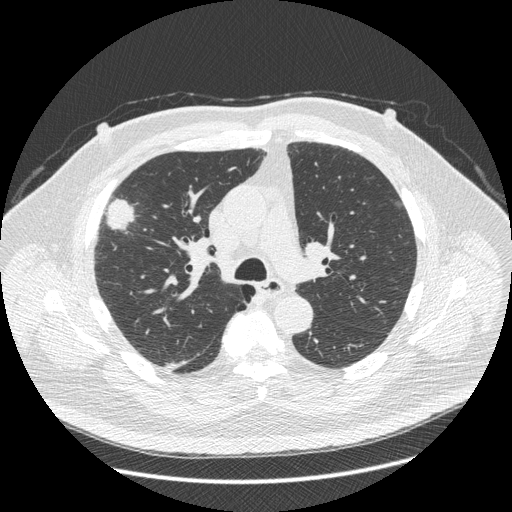
Chest CT (low-dose screening protocol), one axial image; third annual screen; lung window (W 1500 / L -600 HU); standard (soft-tissue) reconstruction kernel (STANDARD); slice 150 of 426 in the series; 512 × 512 image matrix. Male, age 66 years at enrolment. Current smoker at enrolment.
Expert-annotated lung lesion, bounding box [x1, y1, x2, y2] px = [86, 182, 145, 265]. Screening reader's record for this exam (one nodule recorded; not confirmed to be the boxed lesion): non-calcified nodule or mass ≥4 mm, right upper lobe, 48 × 25 mm, spiculated (stellate) margins, soft tissue attenuation, pre-existing on the prior screen: no. Participant outcome: lung cancer diagnosed 35 days after this screen — non-small cell carcinoma, right upper lobe, stage IV (AJCC 6th edition), 50 mm at pathology.